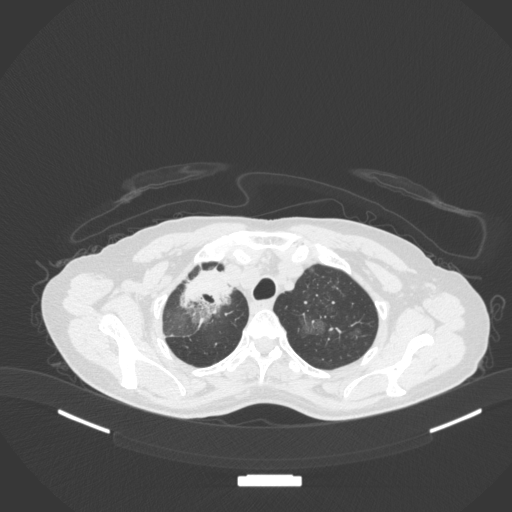
Chest CT, one axial slice. Slice 273 of 311 in the series (ordered by position). 120 kVp. Lung window (W 1500 / L -600 HU). 512 × 512 image matrix. Female patient, age 59 years. Case-level facts recorded for this patient, not image findings: clinical TNM (as recorded): T3 N0 M0; histopathological grade: G1.
Structures marked on this image (bounding box drawn by a radiologist):
- lung tumour (recorded histology: adenocarcinoma): bounding box [x1, y1, x2, y2] px = [176, 258, 238, 322]